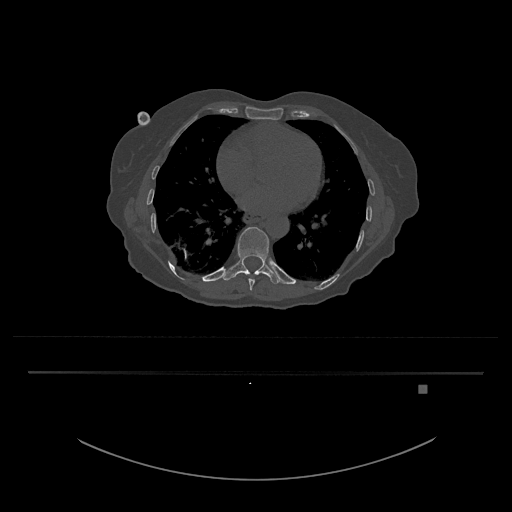
CT including the spine, one axial slice; slice 728 of 797 in the series (ordered by position); reconstruction kernel Br40s/3; 120 kVp; bone window (W 1800 / L 400 HU); 0.5 mm slice thickness; 512 × 512 image matrix, field of view 500 × 500 mm. Patient: female, 57 years. From the clinical record (not read from this slice): primary cancer: cervical.
Annotated regions visible in this slice (semi-automatic segmentation, software-assisted and operator-edited):
- T10 vertebra: box from (x=222, y=227) to (x=283, y=284) px
- T9 vertebra: (x=249, y=279)–(x=255, y=291)